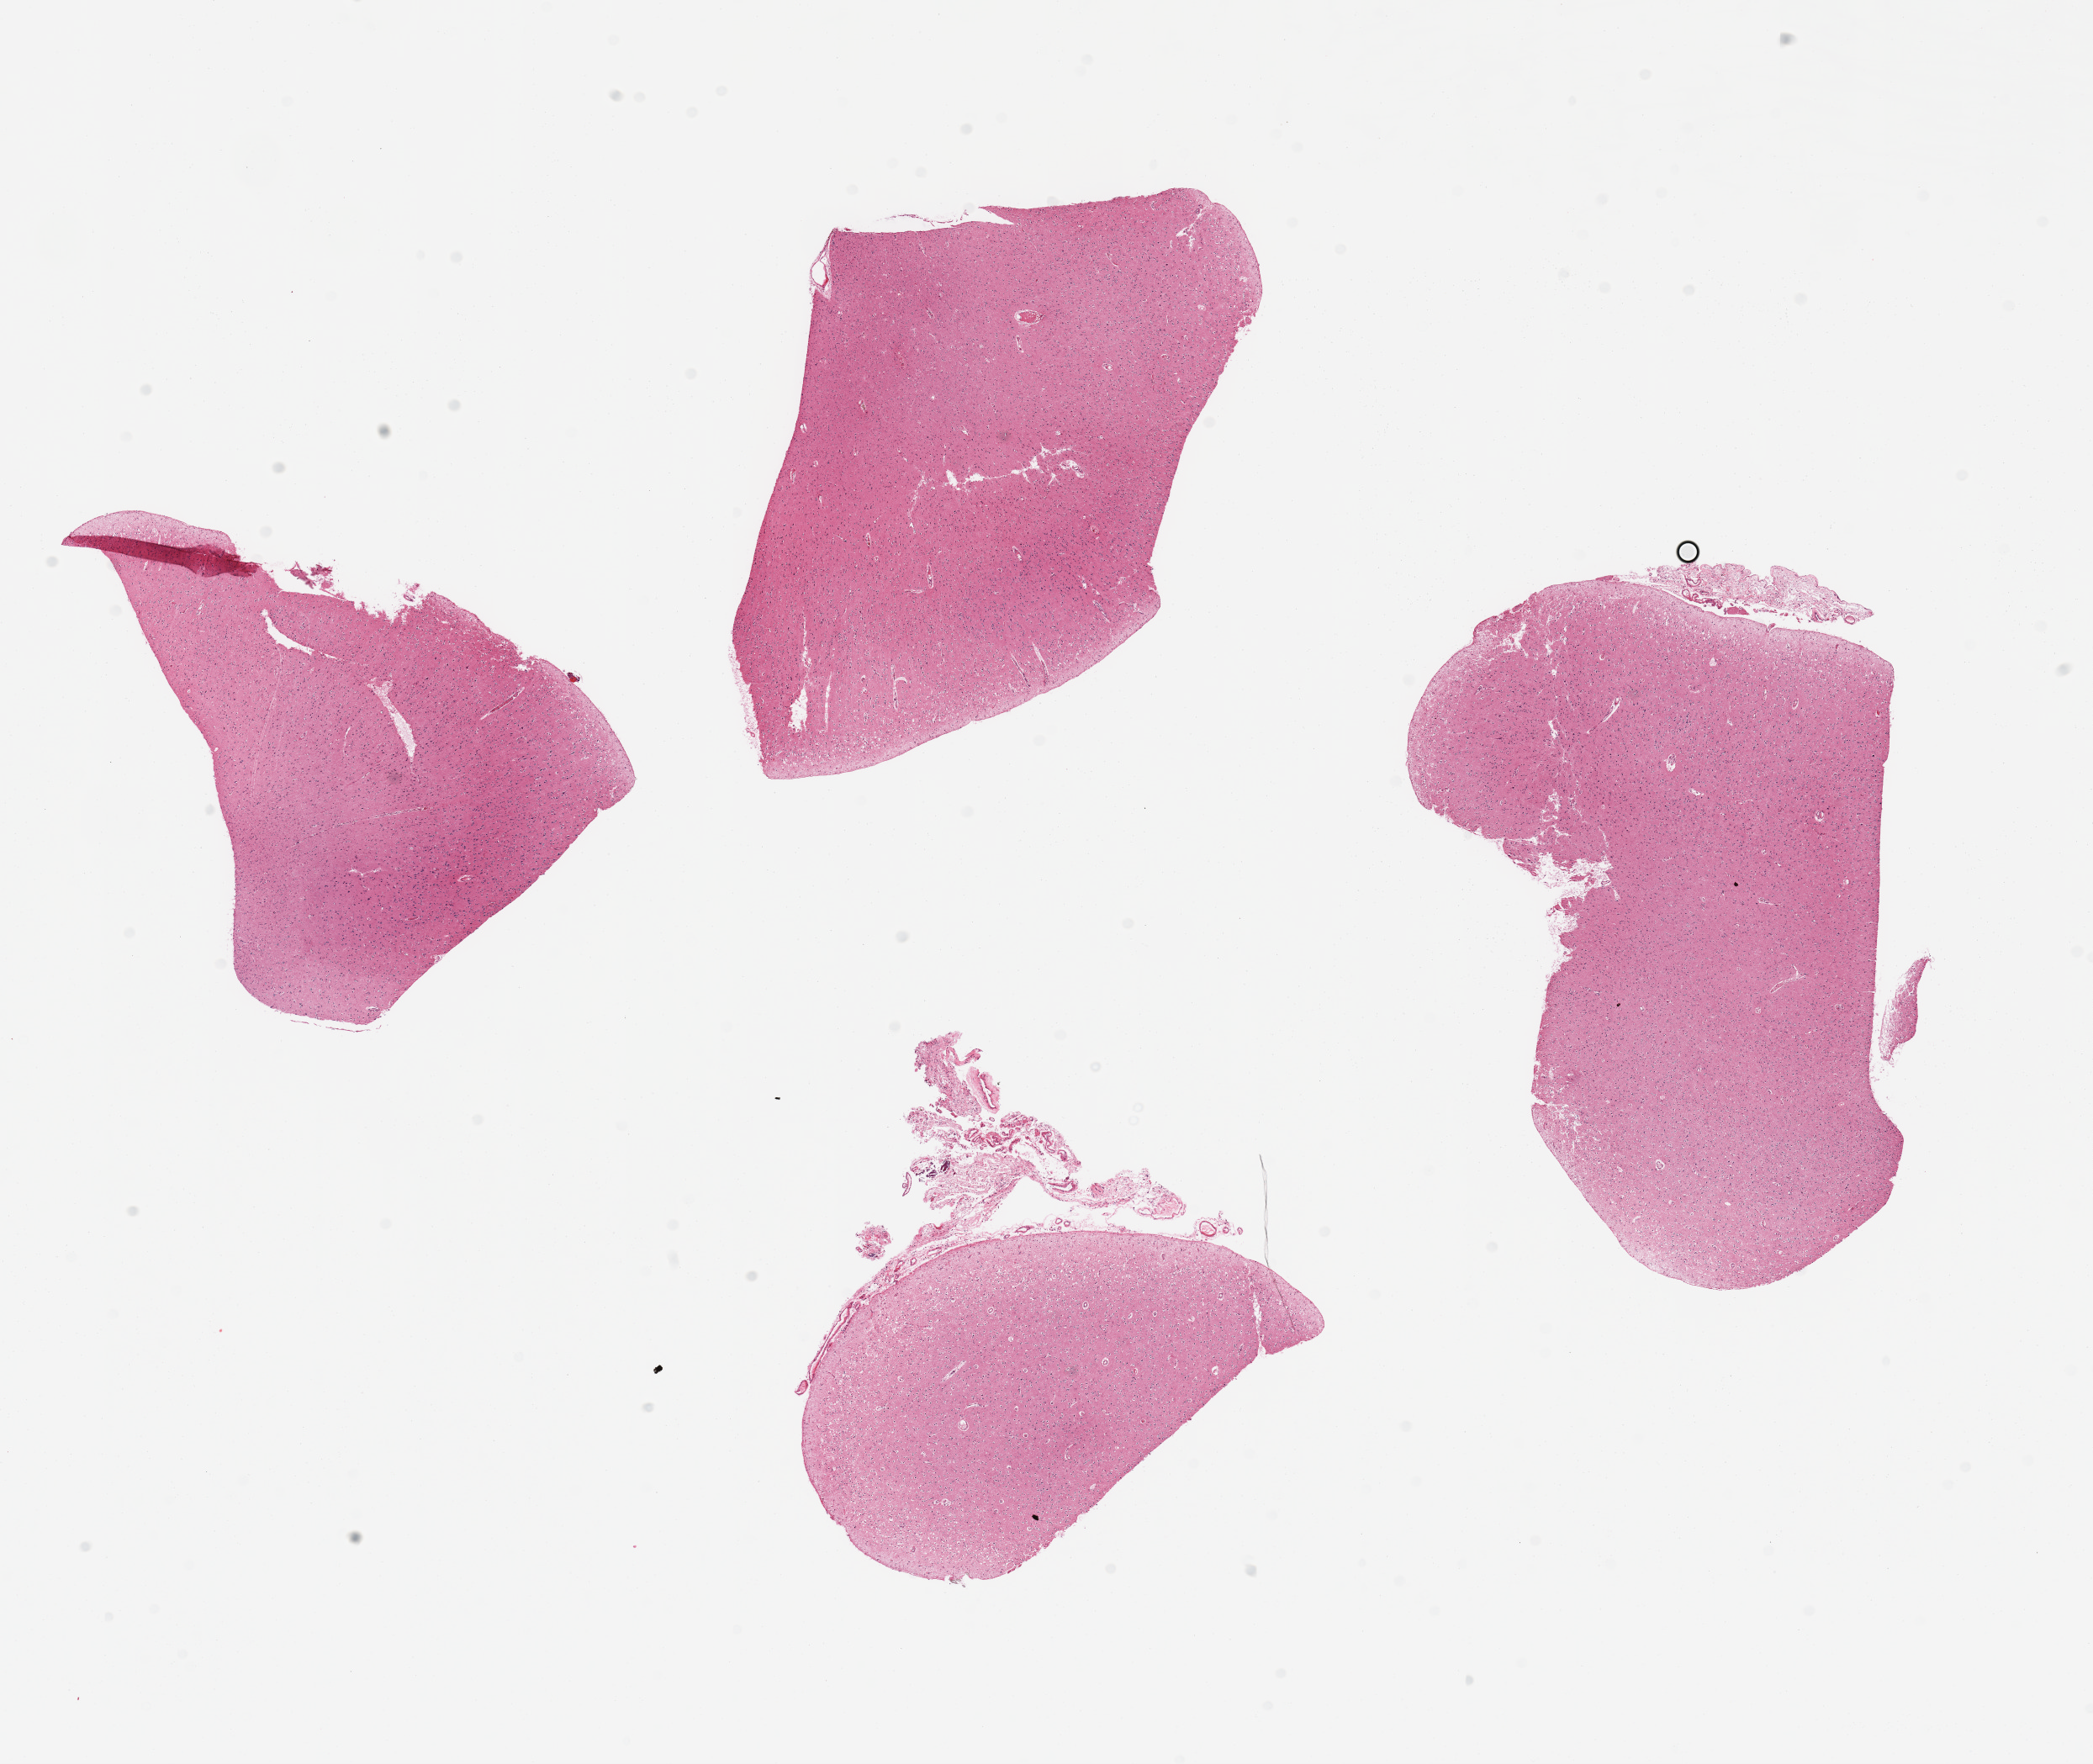
Whole-slide image, H&E stain, brightfield, low-resolution overview of the scanned area, about 19.7 x 16.6 mm; PAXgene-fixed paraffin-embedded (PFPE) section; target tissue: cerebral cortex; donor tissue sample. Female donor.
Reviewer comment on this tissue sample: 4 pieces; adherent meninges on 2 pieces.